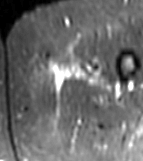
MRI of an extremity soft-tissue mass, one axial slice; position 5 of 81 along the scan axis; STIR; MR volume resampled by the dataset authors to the PET/CT grid (not the native acquisition matrix); 3.27 mm slice thickness; 143 × 161 image matrix. Female patient. From the clinical record (not read from this slice): histological type: myxofibrosarcoma; grade: intermediate; site of the primary tumour: left thigh.
Structures marked on this image (expert contour drawn on MRI and transferred to this co-registered scan by the dataset authors):
- gross tumour volume including surrounding oedema: box from (x=47, y=58) to (x=107, y=91) px